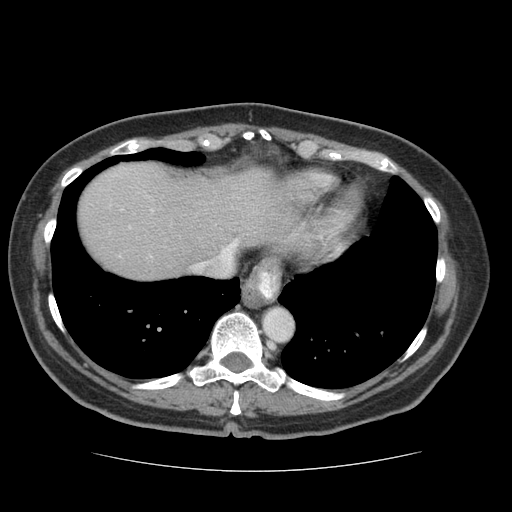
Contrast-enhanced abdominal CT (liver protocol), one axial slice. Position 63 of 75 along the scan axis. 140 kVp. Soft-tissue window (W 400 / L 40 HU). 2.5 mm slice thickness. 512 × 512 image matrix, field of view 360 × 360 mm. From the clinical record (not read from this slice): diagnosis: hepatocellular carcinoma (patient treated with transarterial chemoembolisation; whether this scan precedes or follows treatment is not stated here); TNM stage (as recorded): Stage-I; Child-Pugh class: A; tumour differentiation: moderately differentiated; tumour nodularity: uninodular.
Annotated regions visible in this slice (semi-automatic segmentation, software-assisted and operator-edited):
- liver parenchyma outside the tumour (the mass and vessels are separate outlines, so this box may not span the whole liver): box from (x=78, y=162) to (x=317, y=278) px
- liver vessels: (x=129, y=209)–(x=238, y=247)